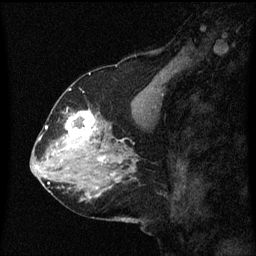
Breast MRI (dynamic contrast-enhanced), one sagittal slice. Dynamic contrast-enhanced series, image 2 of 3 at this slice position (ordered by acquisition). 1.5 T. TE 4.2 ms, TR 8.4 ms. 2 mm slice thickness. 256 × 256 image matrix, field of view 200 × 200 mm. Female patient, age 58 years.
Annotated regions visible in this slice (semi-automatic segmentation, software-assisted and operator-edited):
- analysis volume of interest (the breast-tissue region the enhancement analysis was run in; not a lesion): bounding box <58,110,99,151> (left, top, right, bottom; pixels)
- tumour enhancement mask (voxels above the 70 % enhancement threshold inside the analysis volume of interest): <64,110,97,149>